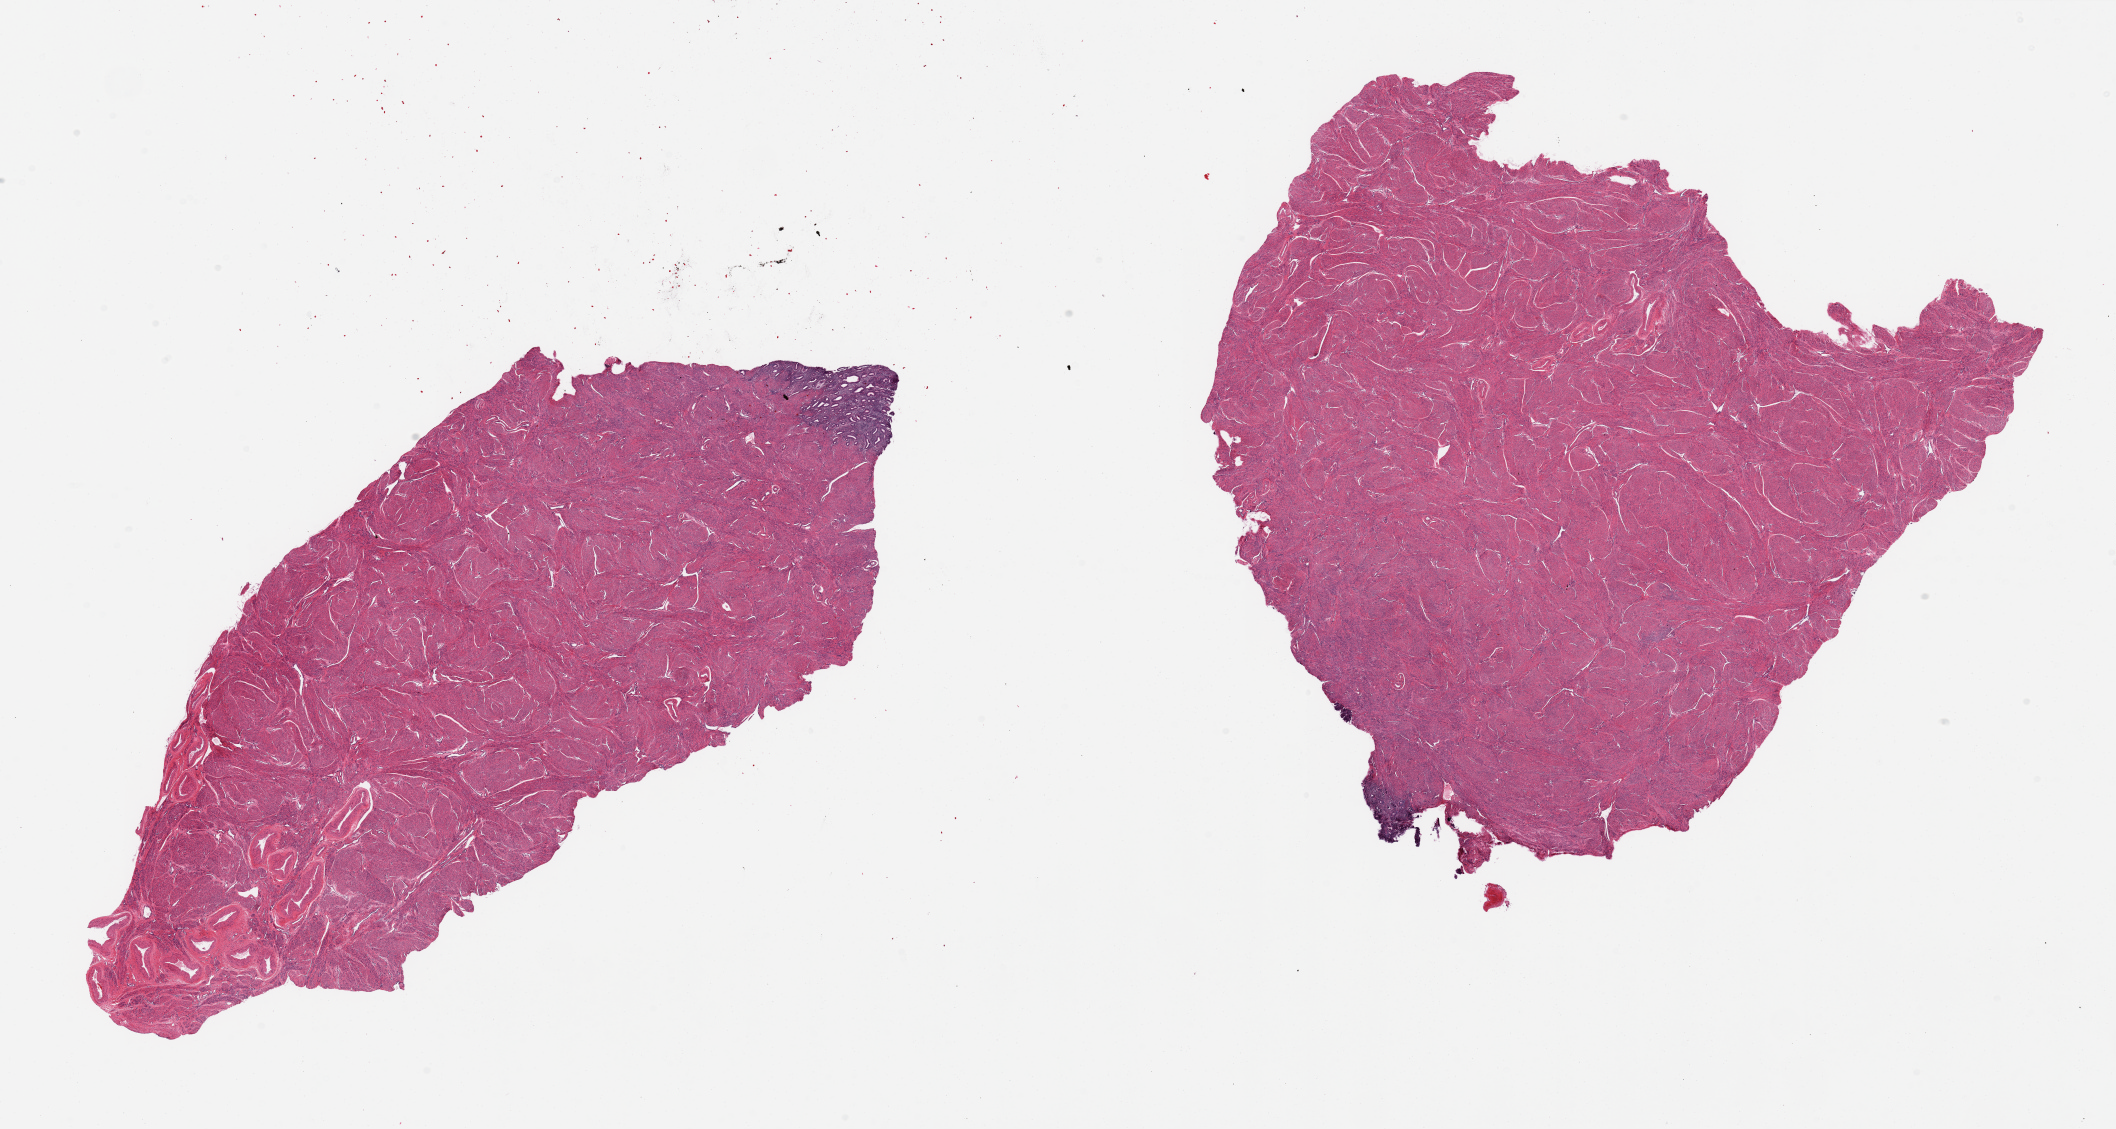
Whole-slide image, H&E stain — low-resolution overview of the scanned area, about 33.5 x 17.9 mm, PAXgene-fixed, paraffin-embedded tissue, target tissue: uterus, tissue donor sample. Donor sex: female.
Review note (as recorded): 2 pieces, predominantly myometrium, small portion of endometrium.